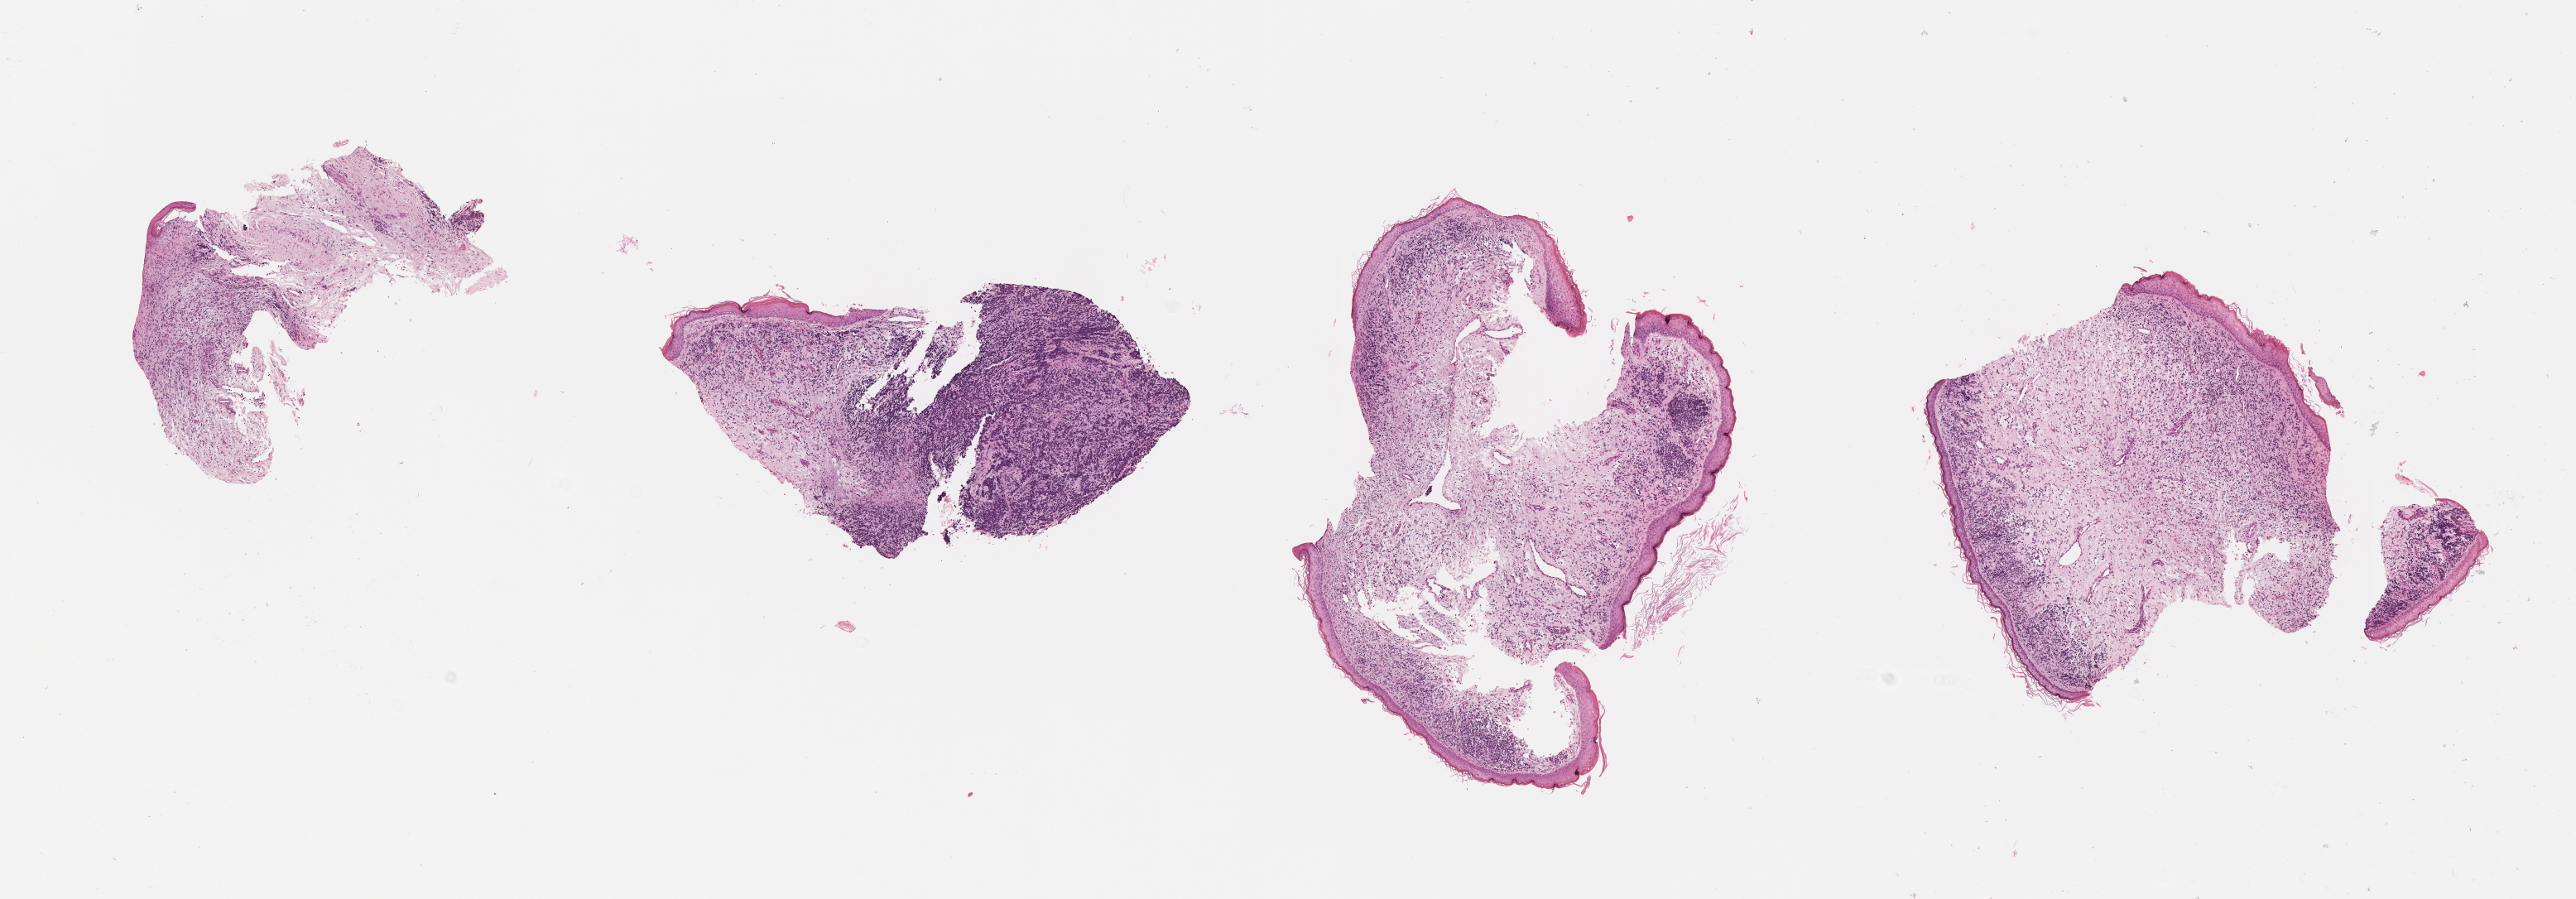
Whole-slide image, hematoxylin and eosin (H&E) stain of tumor tissue, whole scanned area (about 12.6 x 4.4 mm) shown as a low-resolution overview, FFPE section, site: soft tissue, ear-right. Patient: male, age 6.2 years at diagnosis.
Diagnosis: rhabdomyosarcoma; histological classification: embryonal rhabdomyosarcoma. Stage (as recorded): 4. Primary site (case record): middle ear (PM). Metastatic status at presentation (as recorded): metastatic (confirmed).